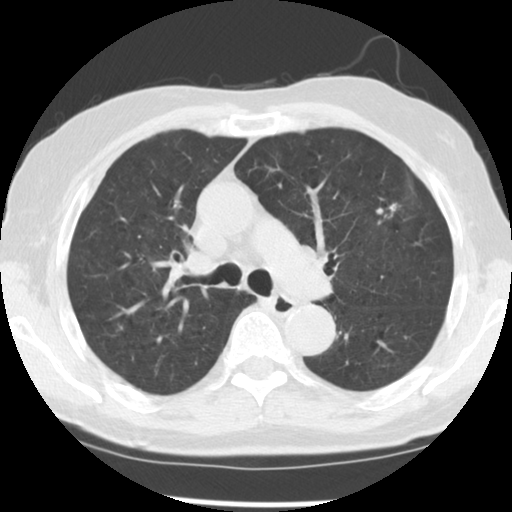
Chest CT (low-dose screening protocol), one axial image; third annual screen; lung window (W 1500 / L -600 HU); 140 kVp; slice 83 of 131 in the series; 512 × 512 image matrix. Male participant, aged 70 years at enrolment.
• Expert reader's lesion annotation, box from (x=355, y=183) to (x=416, y=245) px.
• The screening reader recorded 3 non-calcified nodules or masses ≥4 mm on this exam; which of them this box marks is not recorded.
• Lung cancer was diagnosed 74 days after this screen: adenocarcinoma, NOS, left upper lobe, moderately differentiated (G2), stage IIIA (AJCC 6th edition), 17 mm at pathology.